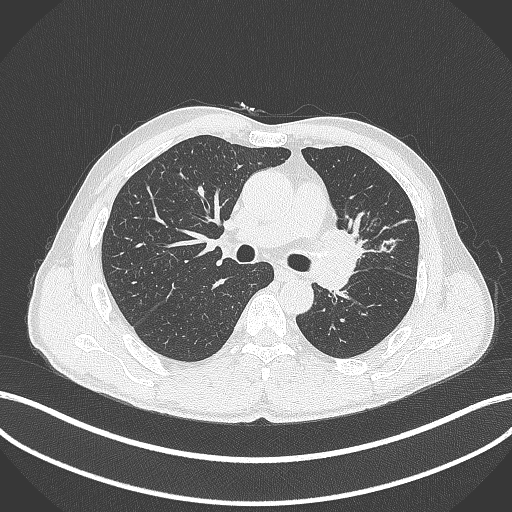
Chest CT, one axial slice; position 255 of 429 along the scan axis; reconstruction kernel B70f; 120 kVp; lung window (W 1500 / L -600 HU); 1 mm slice thickness; 512 × 512 image matrix, field of view 400 × 400 mm. Male patient, age 57 years. From the clinical record (not read from this slice): clinical TNM (as recorded): T2b N0 M0.
Outlined on this slice (rectangle marked by the reading radiologist):
- lung tumour (recorded histology: squamous cell carcinoma): bounding box [x1, y1, x2, y2] px = [319, 226, 369, 263]